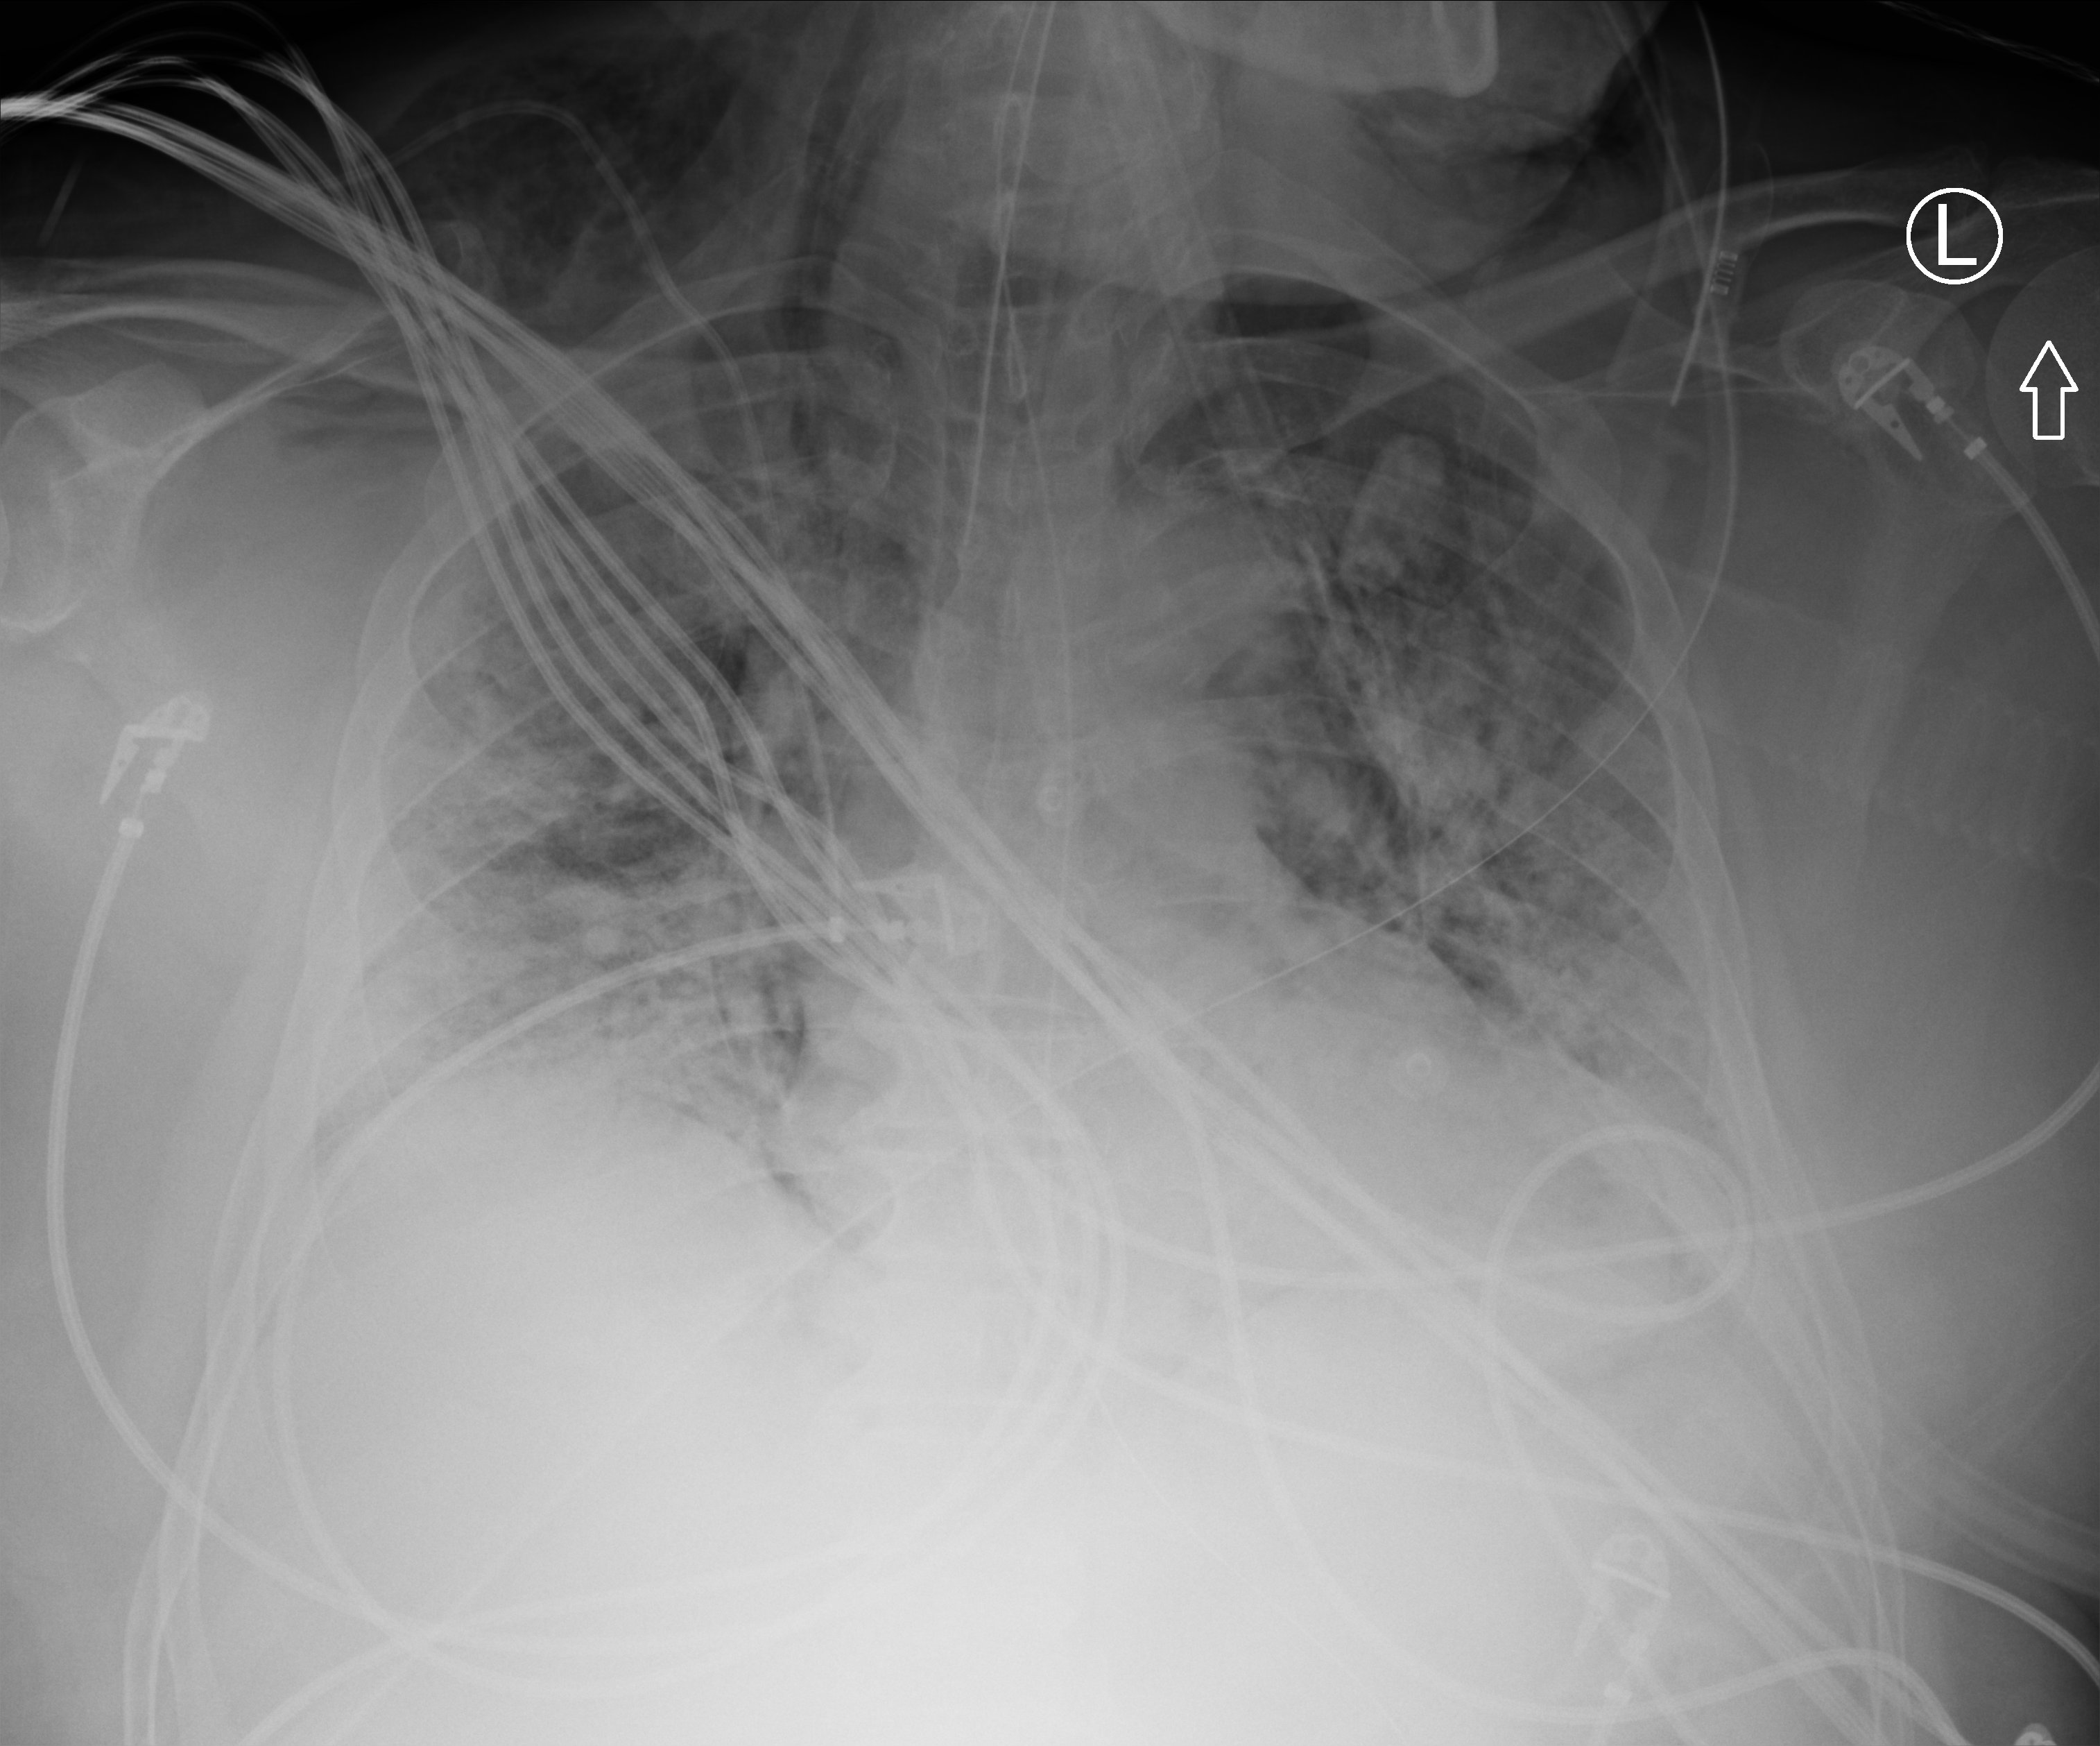
Bedside chest radiograph (computed radiography). Adult patient hospitalised with COVID-19, age 18–59 years.
Admission-level facts for this patient (not findings on this image; timing relative to this image not recorded): mechanically ventilated during this hospital stay: yes; admitted to intensive care during this hospital stay: yes.